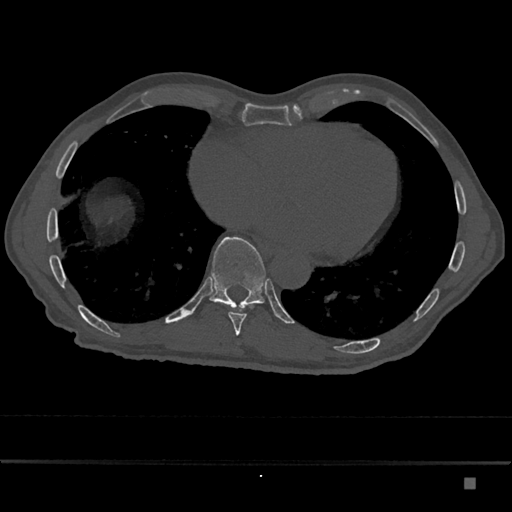
CT including the spine, one axial slice. Position 772 of 797 along the scan axis. Reconstruction kernel Br40s/3. 120 kVp. Bone window (W 1800 / L 400 HU). 0.5 mm slice thickness. 512 × 512 image matrix, field of view 390 × 390 mm. Patient: male, 72 years. Case-level facts recorded for this patient, not image findings: primary cancer: prostate.
Annotated regions visible in this slice (semi-automatically segmented with operator editing):
- T10 vertebra: box from (x=209, y=237) to (x=266, y=310) px
- T9 vertebra: (x=228, y=305)–(x=252, y=336)